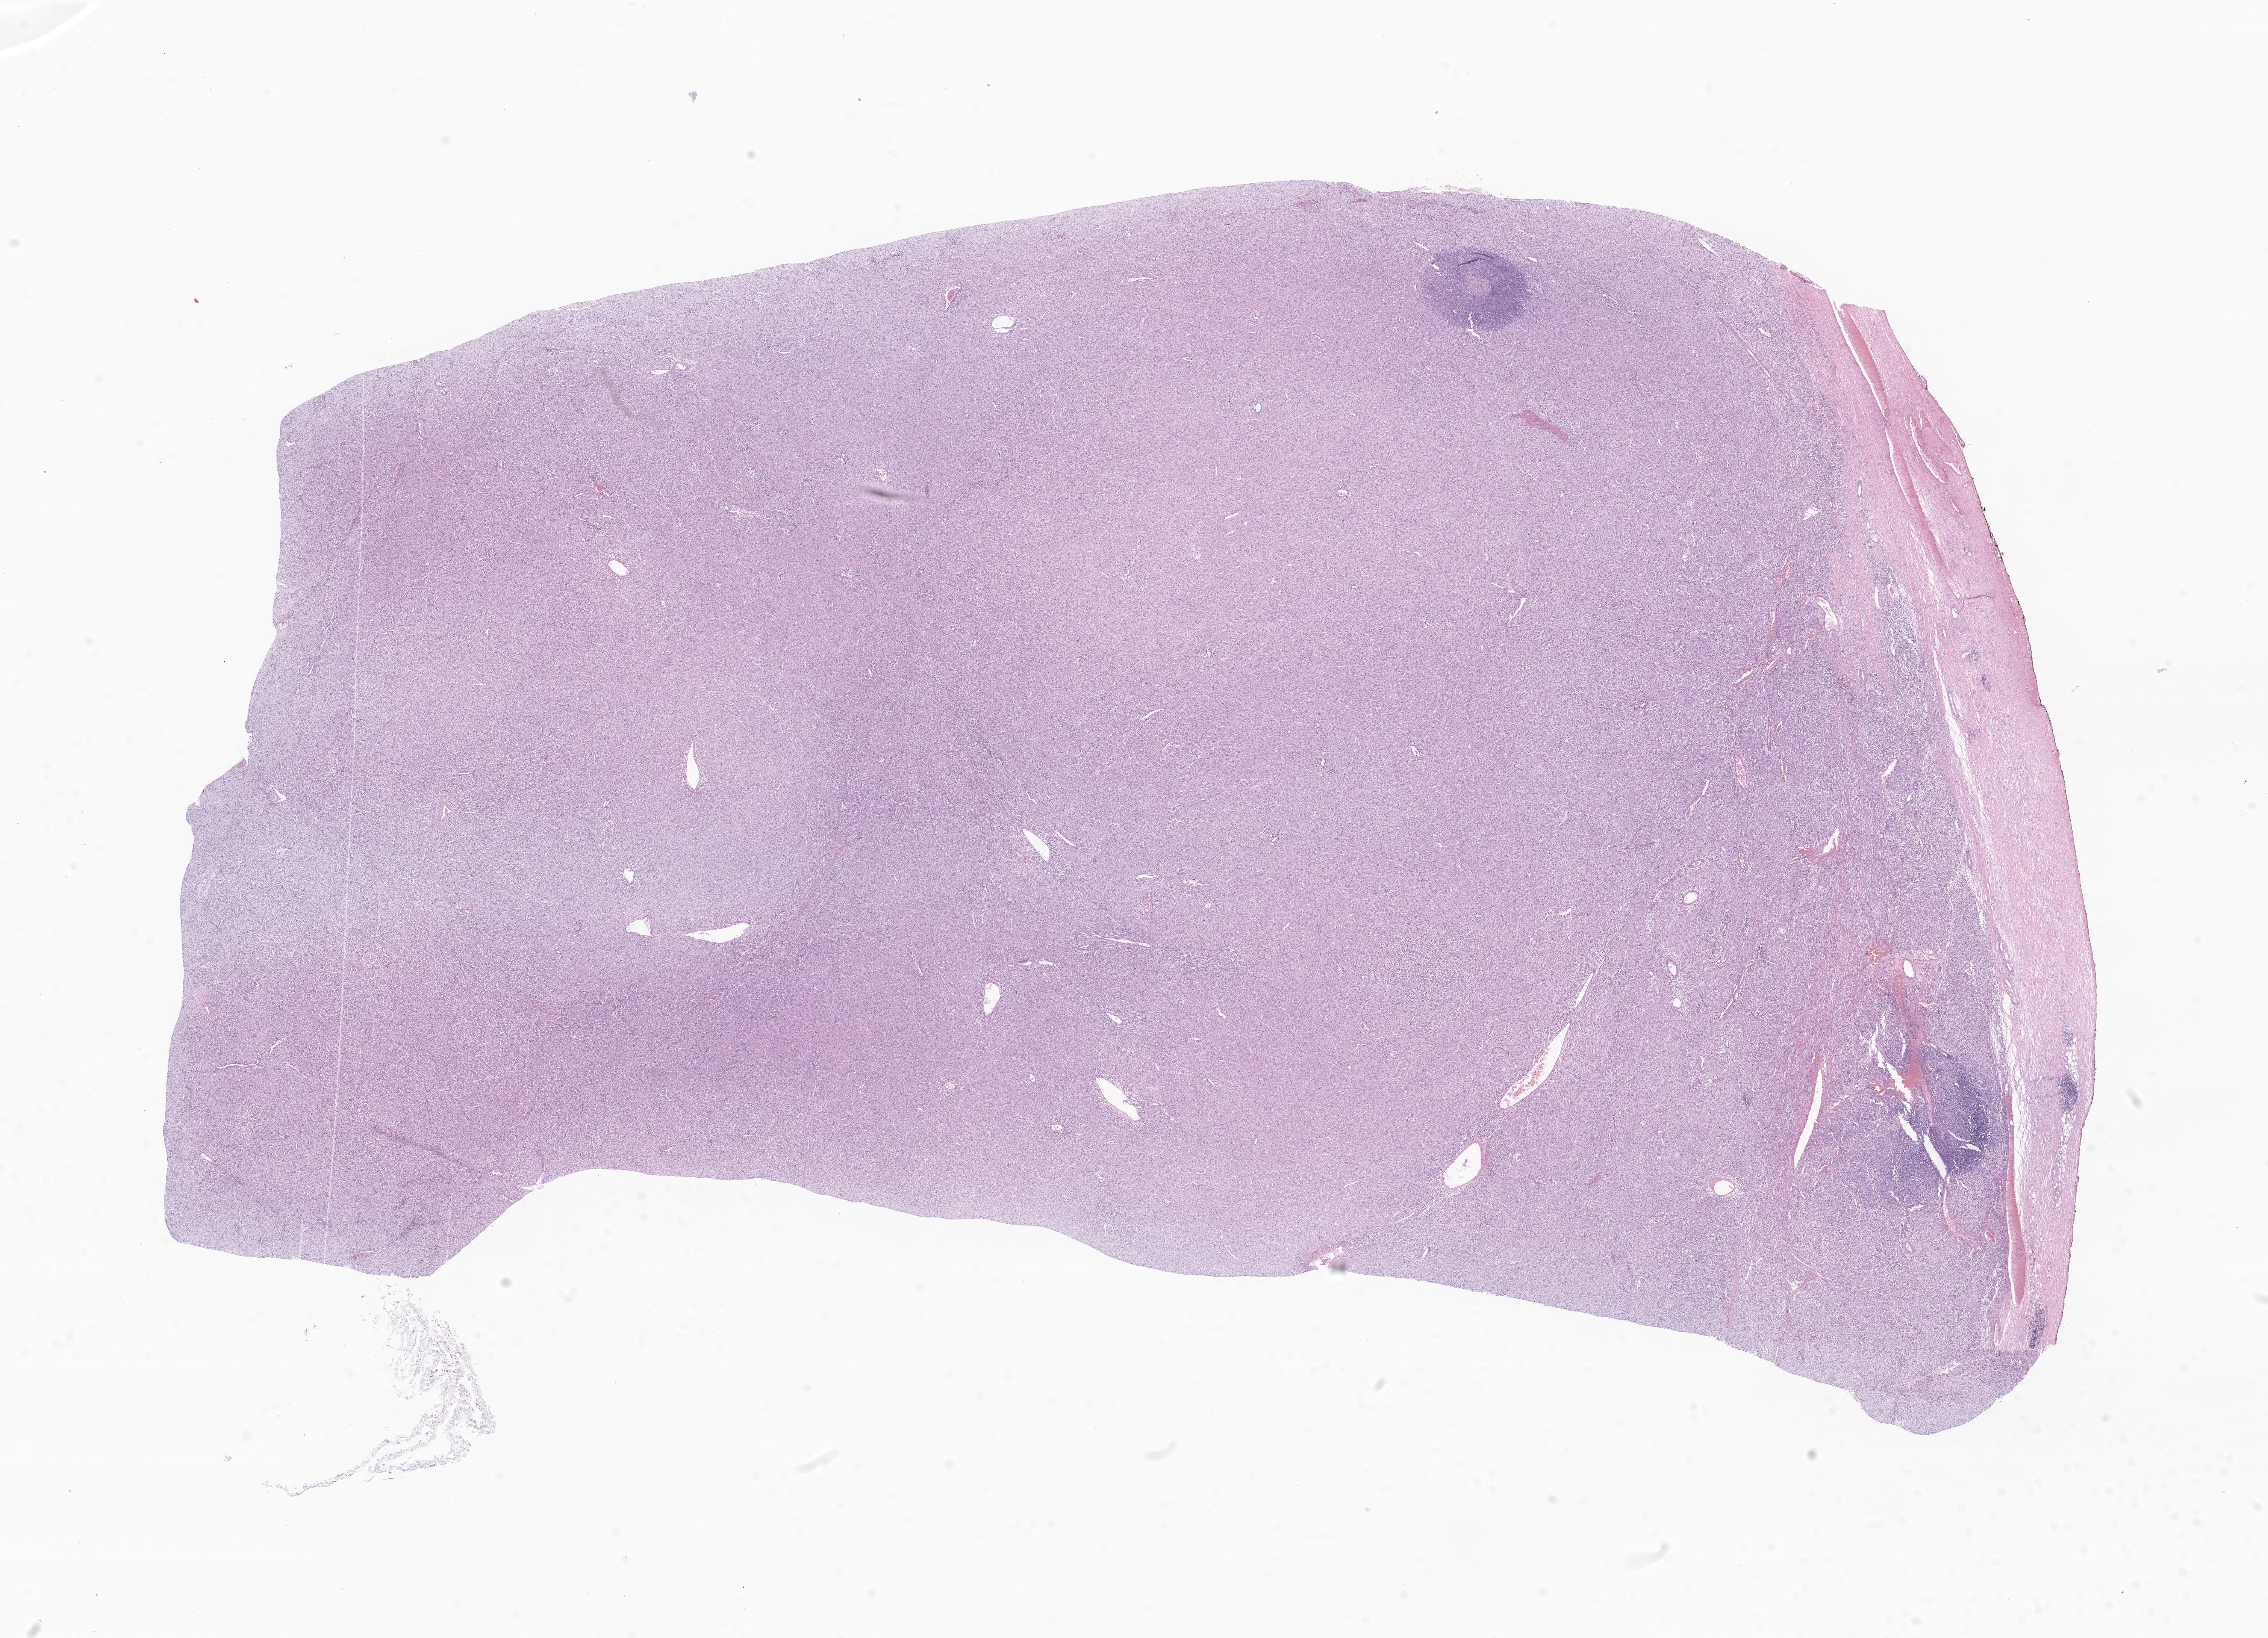
Digitized H&E-stained section of tumor tissue from the abdomen, shown as a low-resolution overview of the whole scanned area (about 25.4 x 18.4 mm); formalin-fixed paraffin-embedded section. Male patient, age 175 months (14 years 7 months).
Recorded diagnosis: Myofibroblastic tumor, NOS.